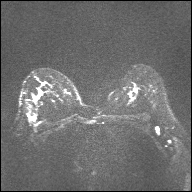
Breast MRI, one axial slice; position 21 of 32 along the scan axis; diffusion-weighted series; image 2 of 4 stored at this slice position (different b-values; order by instance number); 1.5 T; 192 × 192 image matrix, field of view 360 × 360 mm. Female patient.
Structures marked on this image (manually delineated by an expert):
- tumour on diffusion-weighted imaging: bounding box <35,92,41,99> (left, top, right, bottom; pixels)